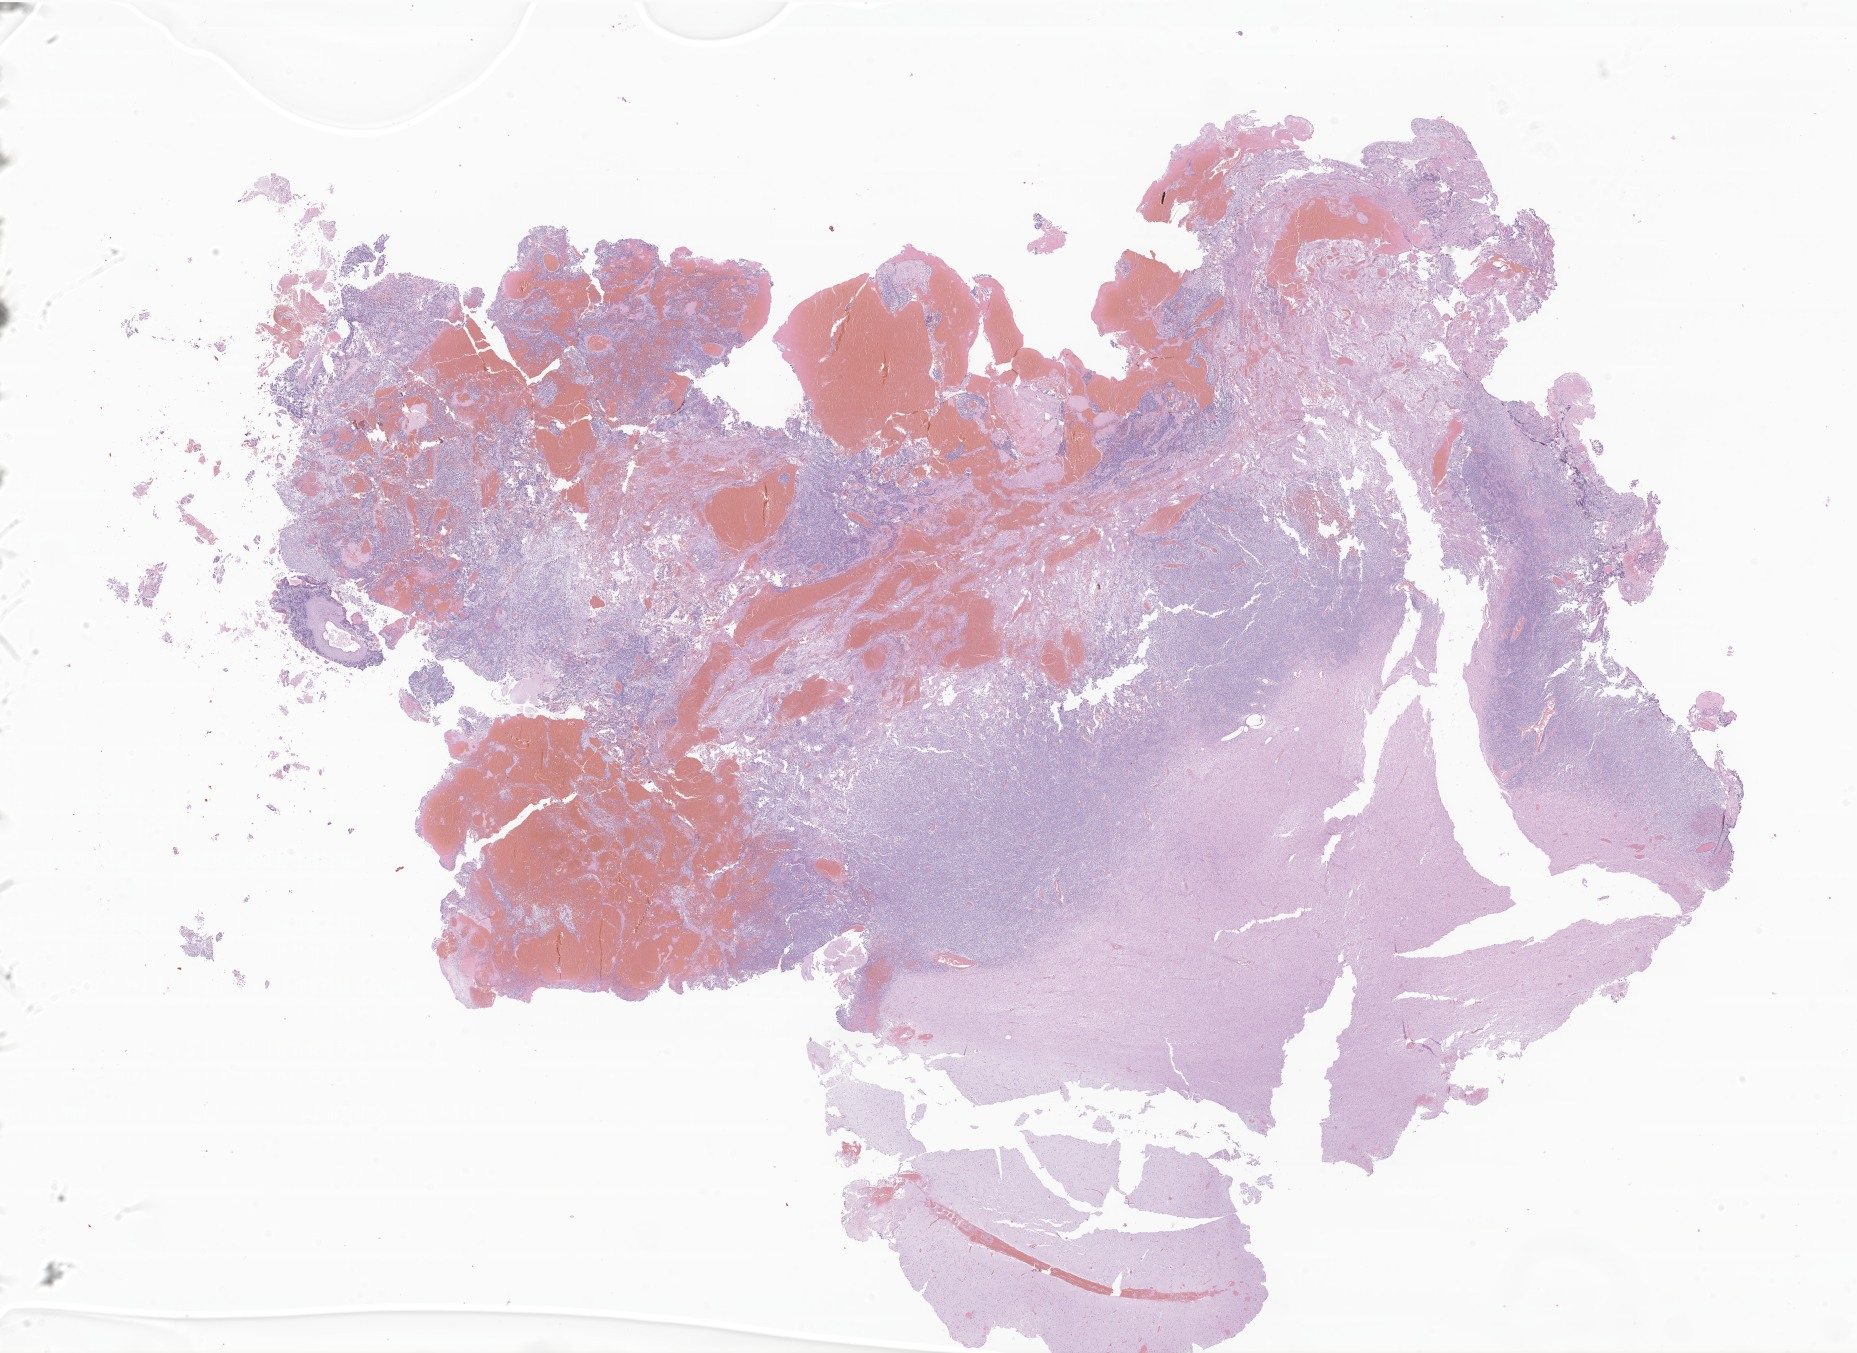
Whole-slide image, haematoxylin and eosin stain of tumor tissue from the frontal lobe — shown as a low-resolution overview of the whole scanned area (about 31.3 x 22.8 mm). Formalin-fixed paraffin-embedded section. Patient: female, age 47 months (3 years 11 months).
• diagnosis: CNS embryonal tumor, NOS